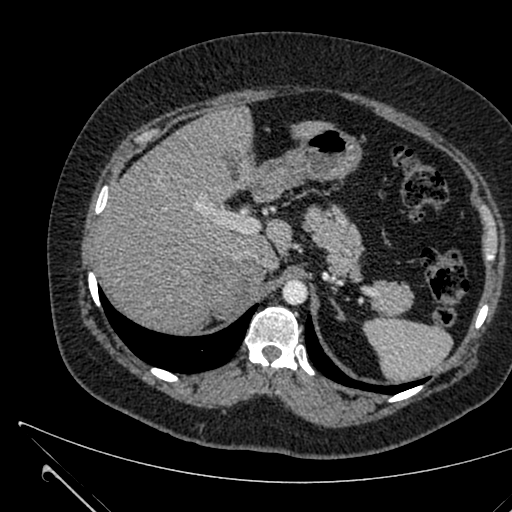
Contrast-enhanced abdominal CT, one axial slice. Slice 473 of 731 in the series (ordered by position). Intravenous contrast given. Soft-tissue window (W 400 / L 40 HU). 512 × 512 image matrix, field of view 376 × 376 mm. Patient: female, 36 years. Case-level facts recorded for this patient, not image findings: diagnosis: adrenocortical carcinoma; tumour side: right adrenal; tumour size at pathology: 10 cm; Ki-67 index: 20 %; stage (as recorded): 4.
Outlined on this slice (semi-automatically segmented with operator editing):
- mass: bounding box [x1, y1, x2, y2] px = [206, 261, 262, 318]